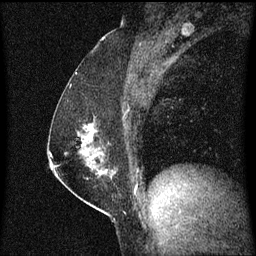
Breast MRI (dynamic contrast-enhanced), one sagittal slice. Slice 35 of 60 in the series (ordered by position). Dynamic contrast-enhanced series, image 2 of 3 at this slice position (ordered by acquisition). 1.5 T. TE 4.2 ms, TR 8.4 ms. 2 mm slice thickness. 256 × 256 image matrix, field of view 200 × 200 mm. Female patient, age 52 years. Case-level facts recorded for this patient, not image findings: setting: breast cancer imaged before/during neoadjuvant chemotherapy; receptor status: HER2-positive.
Structures marked on this image (semi-automatically segmented with operator editing):
- analysis volume of interest (the breast-tissue region the enhancement analysis was run in; not a lesion): bounding box (x1, y1, x2, y2) in pixels: (67, 120, 108, 179)
- tumour enhancement mask (voxels above the 70 % enhancement threshold inside the analysis volume of interest): (90, 132, 95, 137)